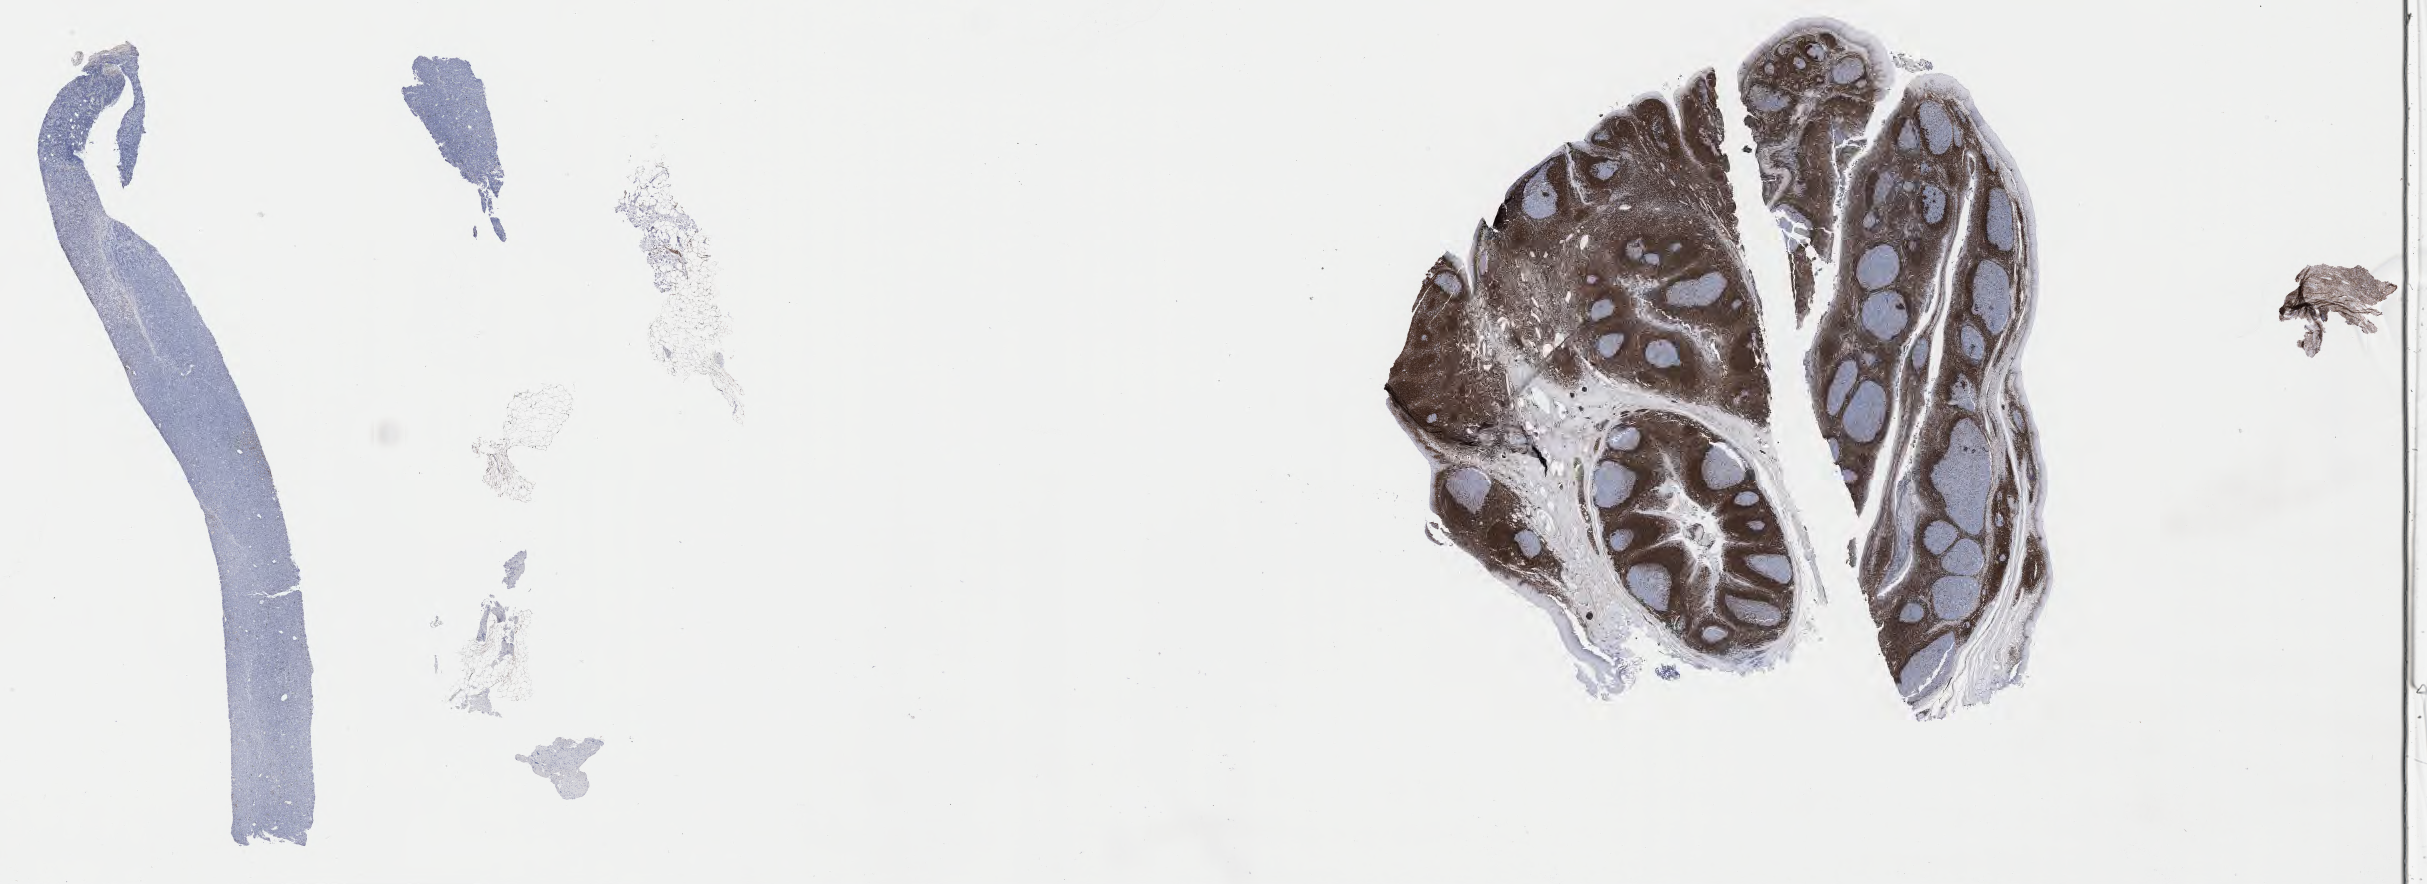
Immunohistochemistry (IHC) whole-slide image stained for BCL2, whole scanned area (about 39.3 x 14.3 mm) shown as a low-resolution overview. Specimen: tumor tissue. Patient: female, 61 years old.
Diagnosis: Burkitt lymphoma, NOS.